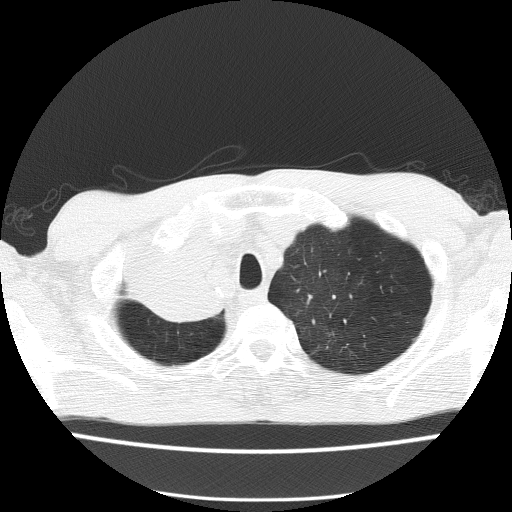
Low-dose screening chest CT, one axial slice. Position 126 of 150 along the scan axis. Reconstruction kernel FC51. 120 kVp. Lung window (W 1500 / L -600 HU). 512 × 512 image matrix.
Structures marked on this image (outlined manually by an expert reader):
- lesion 1 (tumor, hilum of right lung): bounding box <126,247,223,320> (left, top, right, bottom; pixels)